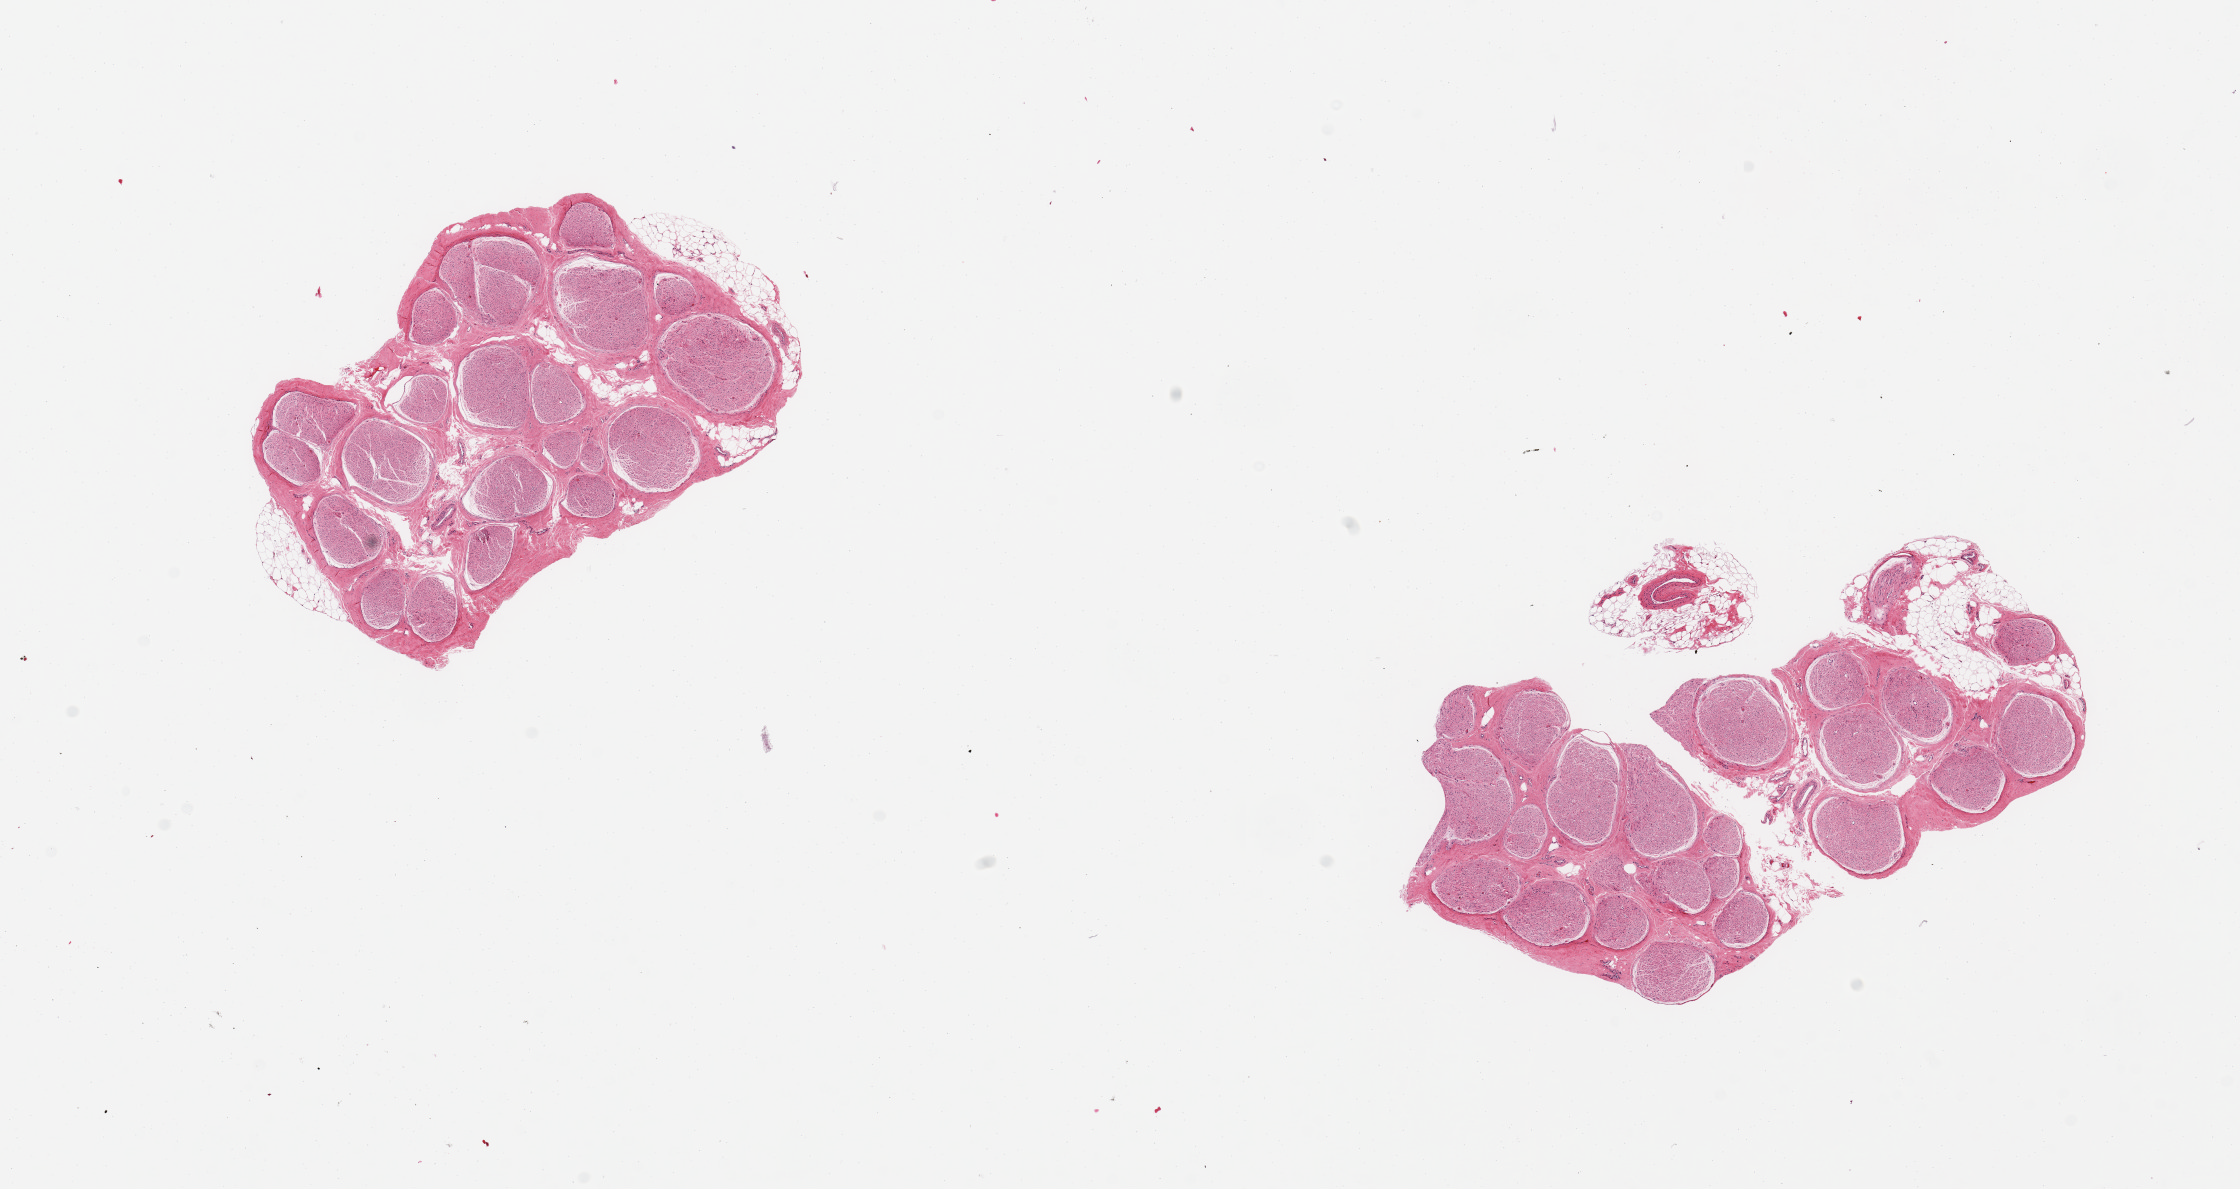
H&E whole-slide image — shown as a low-resolution overview of the whole scanned area (about 17.7 x 9.4 mm, from a 20x scan); PAXgene-fixed paraffin-embedded (PFPE) section; sampled site (target tissue): tibial nerve; tissue donor sample. Female donor.
Pathologist's review note for this sample: 2 pieces, trace nubbins of adherent fat up to ~0.5-1mm.